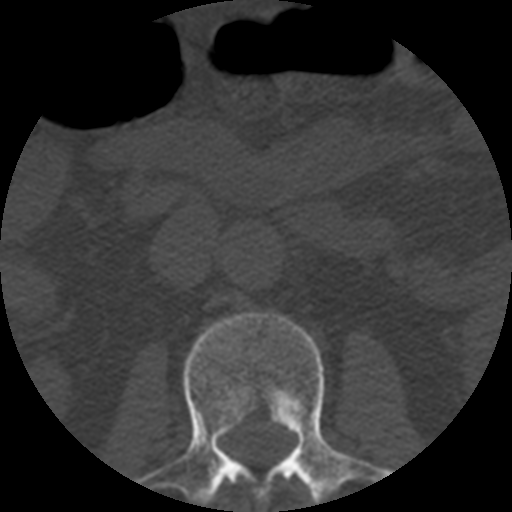
CT including the spine, one axial slice. Slice 154 of 508 in the series (ordered by position). 120 kVp. Bone window (W 1800 / L 400 HU). 1.25 mm slice thickness. 512 × 512 image matrix, field of view 160 × 160 mm. Patient age 57 years. Case-level facts recorded for this patient, not image findings: primary cancer: prostate.
Outlined on this slice (semi-automatic segmentation, software-assisted and operator-edited):
- L2 vertebra: bounding box <137,312,392,504> (left, top, right, bottom; pixels)